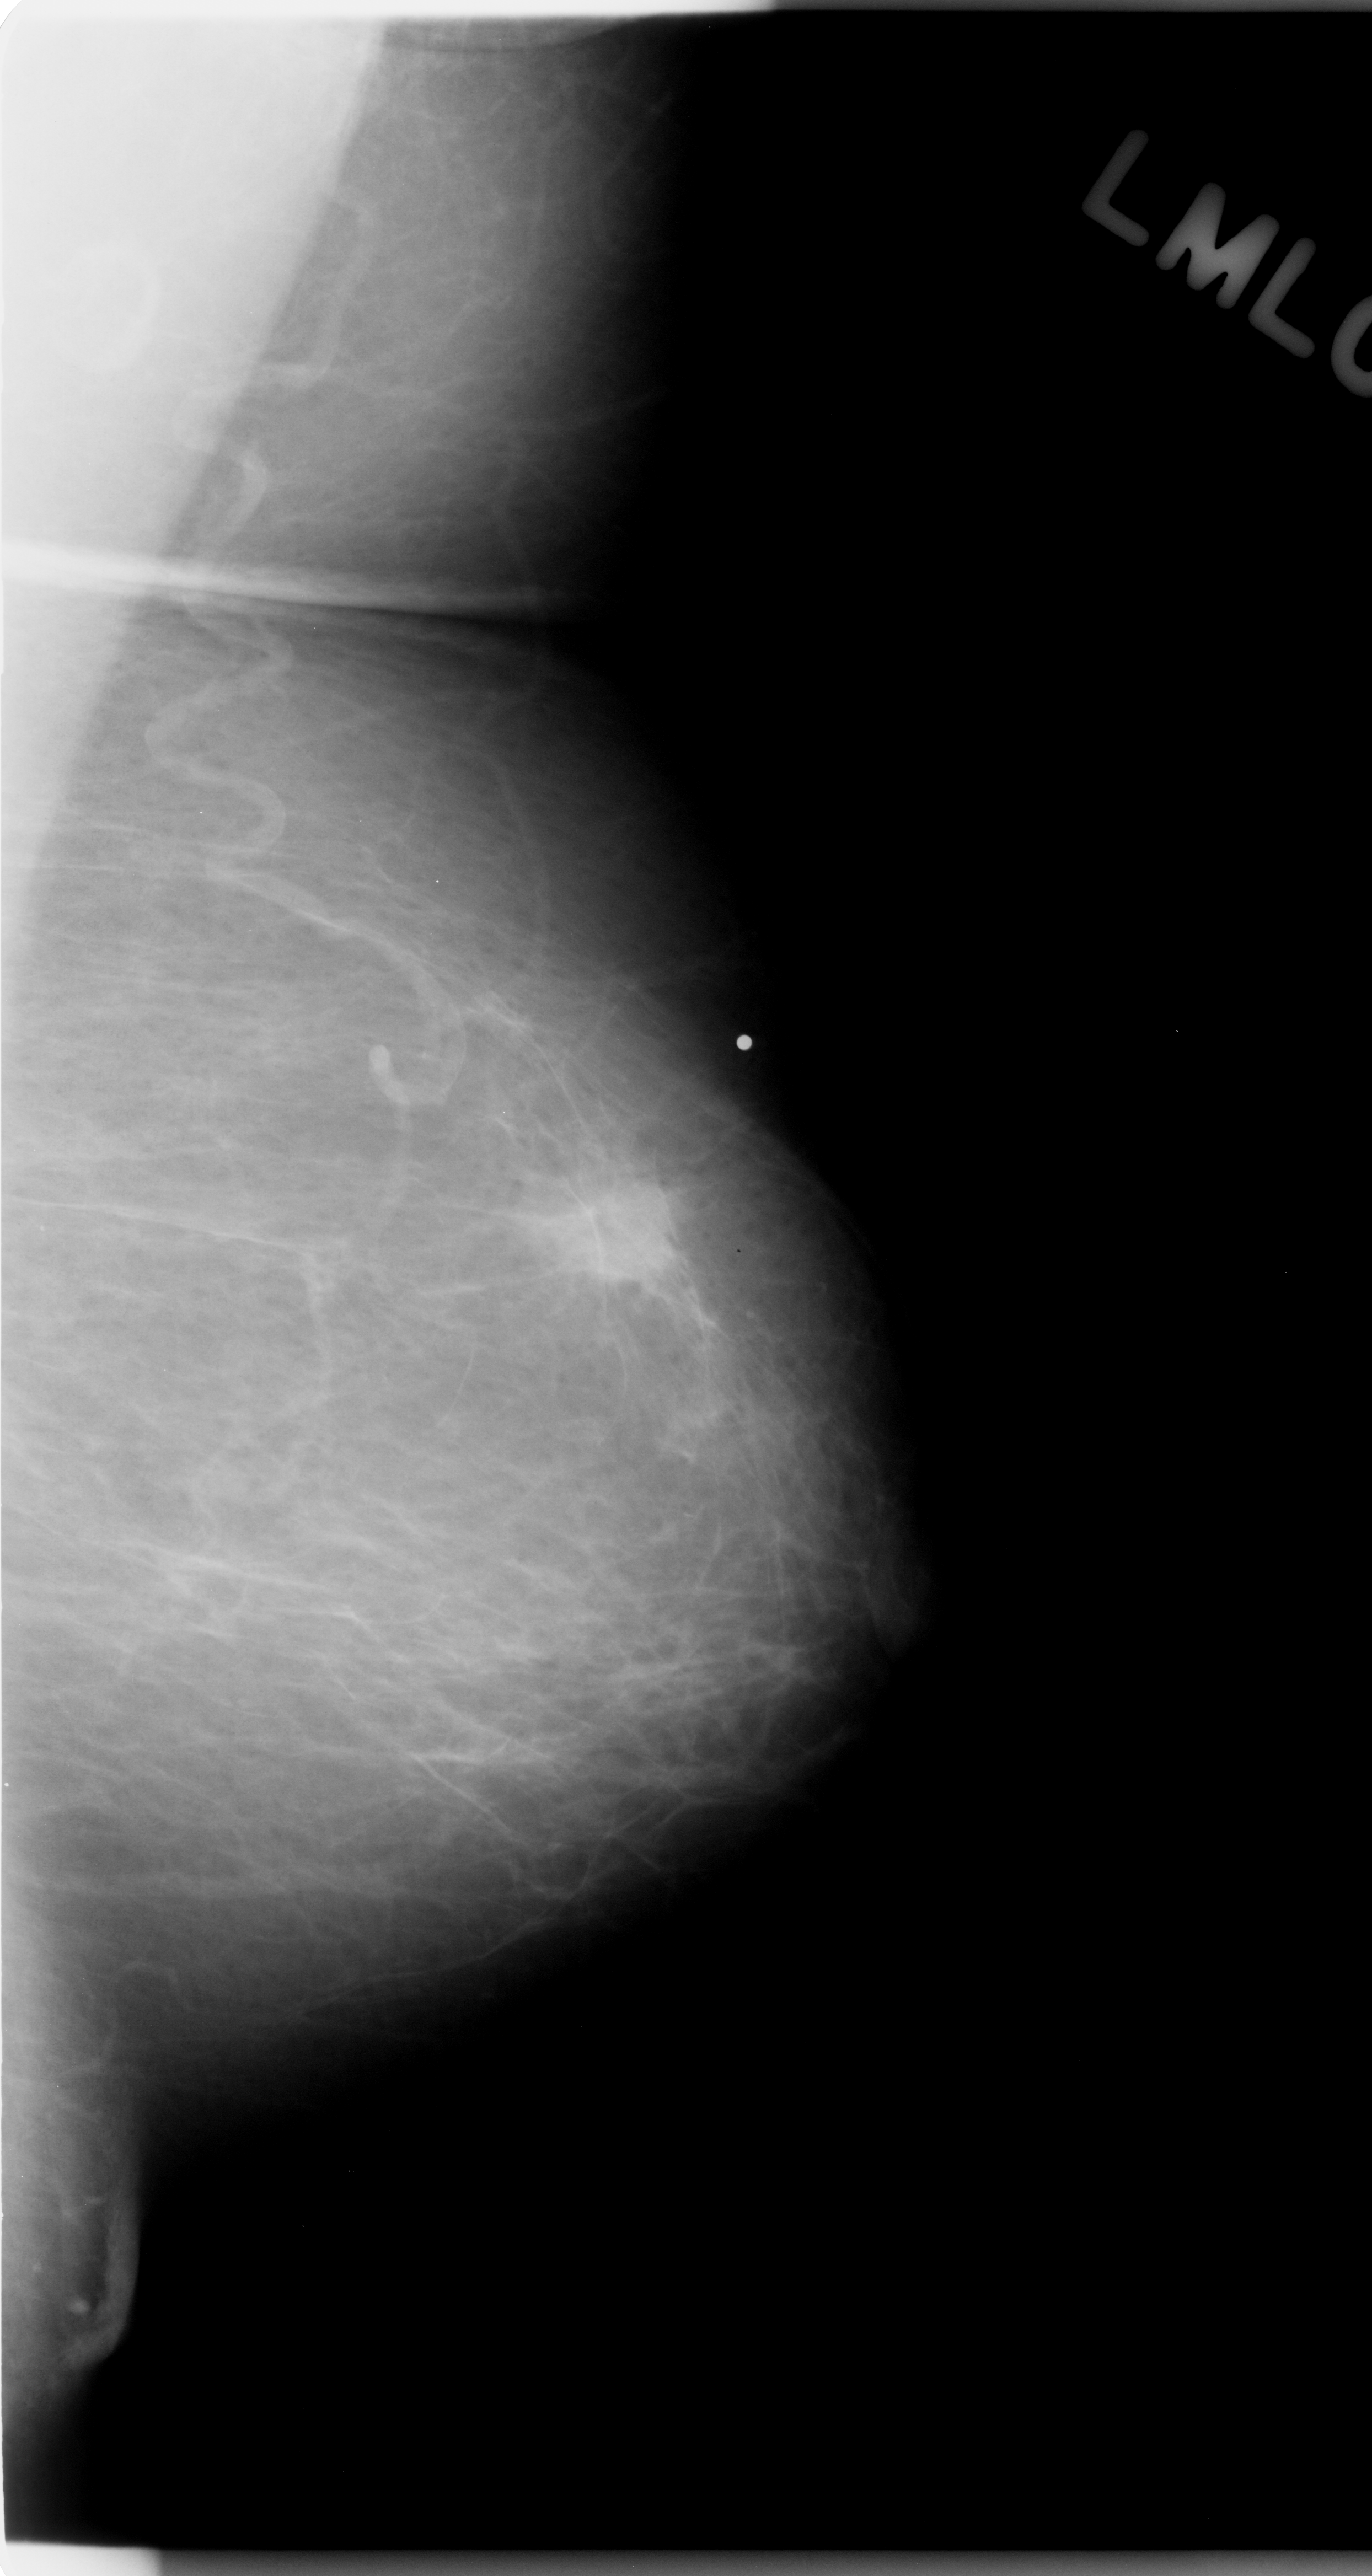
Scanned film-screen mammogram; left breast; mediolateral oblique (MLO) view; 1372 × 2576 image matrix.
Marked abnormalities (boxes around the expert regions of interest):
- mass, shape irregular, margins ill defined; BI-RADS assessment category 5; pathology (as recorded): malignant: box from (x=501, y=1158) to (x=697, y=1330) px